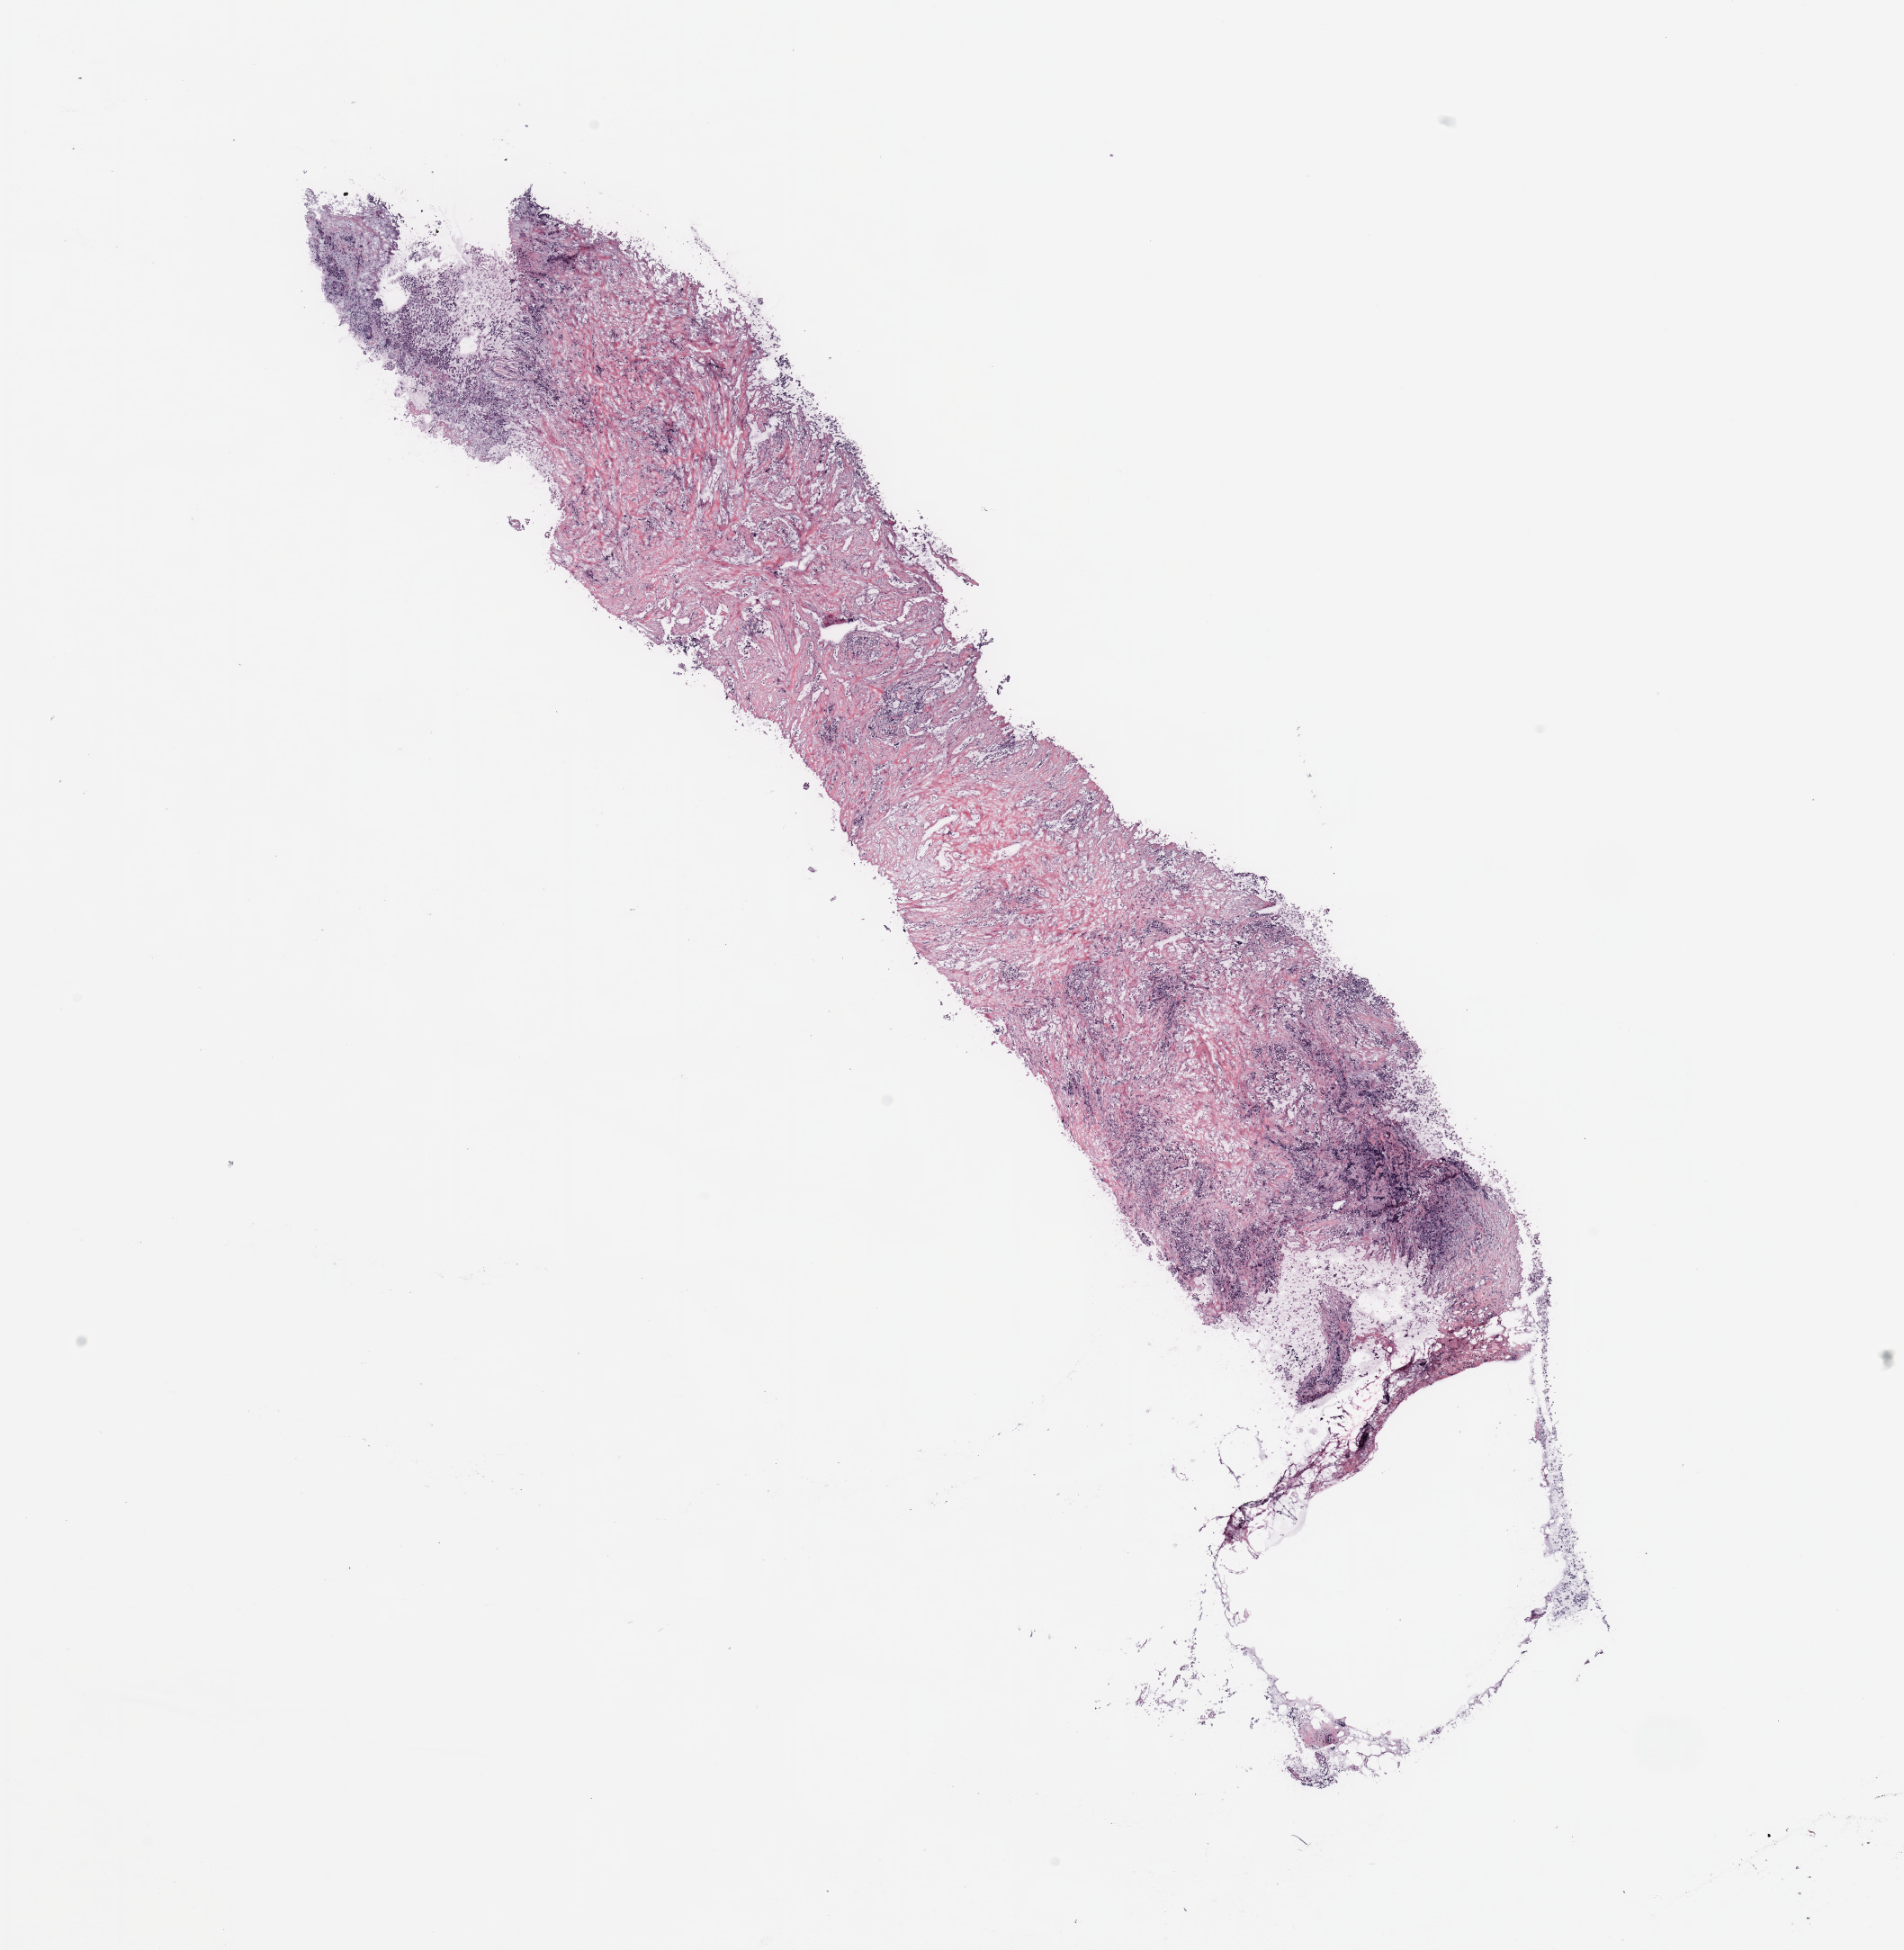
Whole-slide histology image, H&E-stained, a low-resolution overview of the entire scanned area, about 16.7 x 17.1 mm, breast, tissue type not recorded.
Patient diagnosis (cohort enrolment): breast cancer (breast).